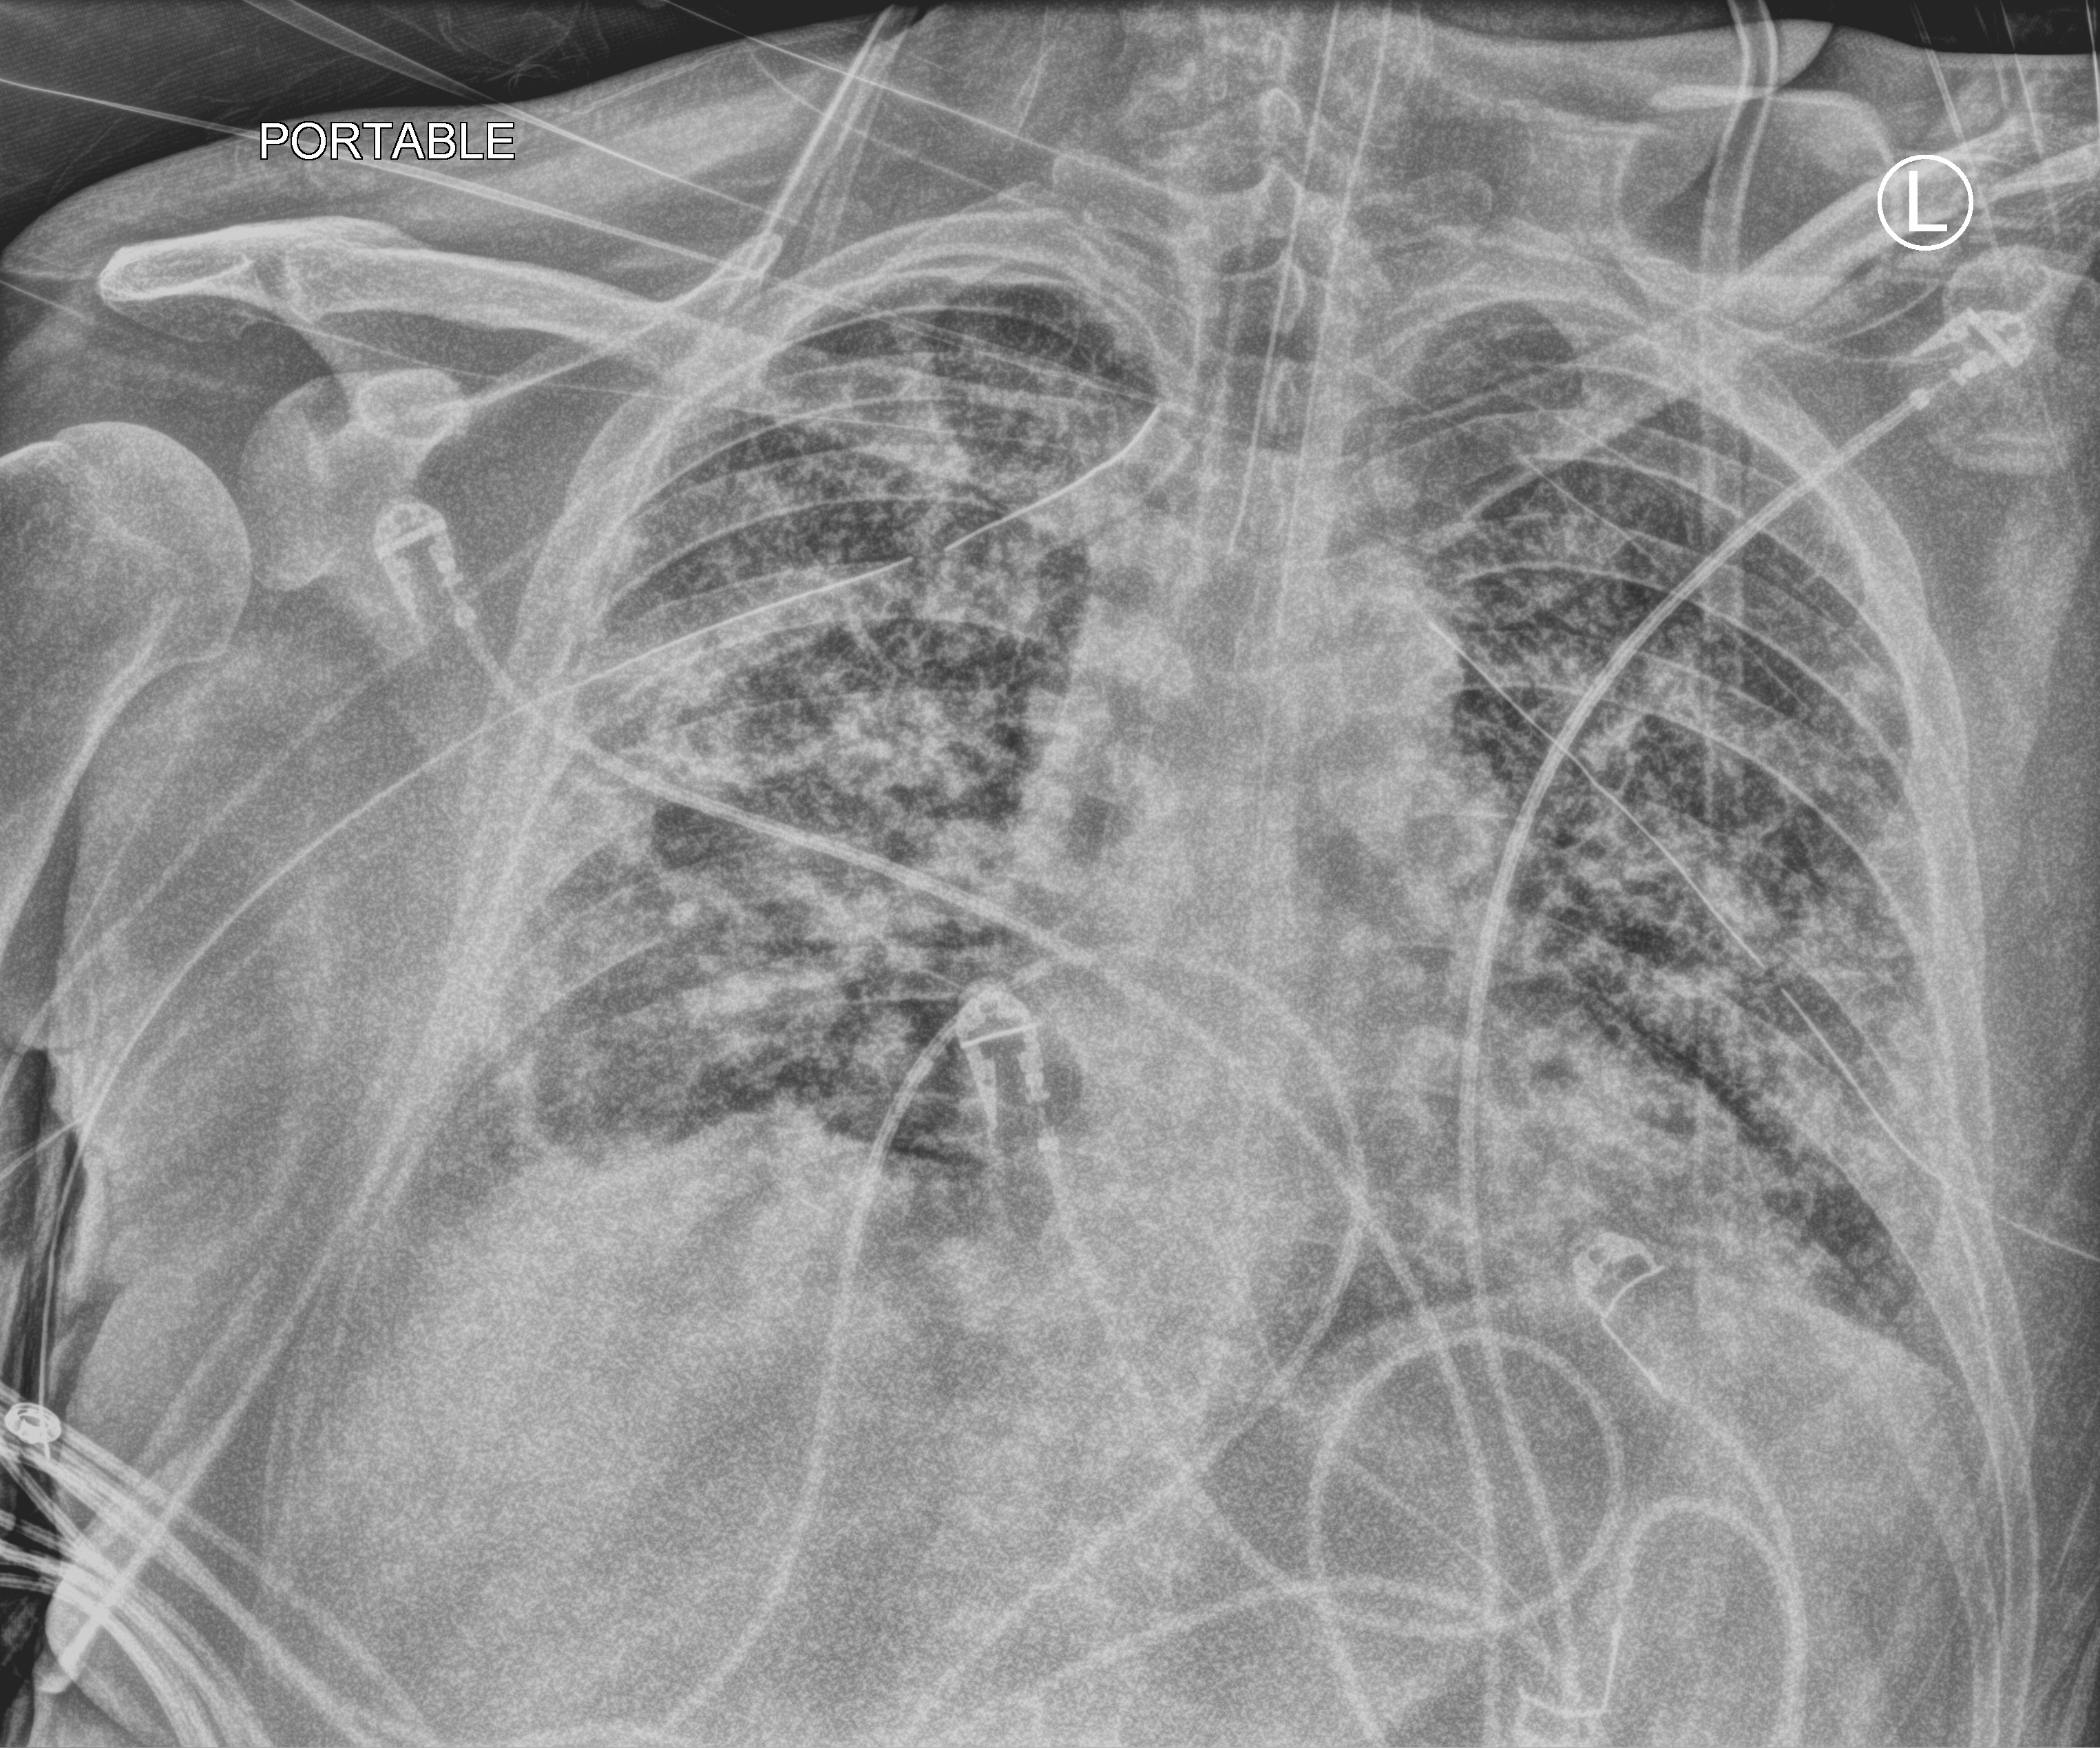
Portable chest radiograph; anteroposterior (AP) projection. Patient hospitalised with COVID-19; male, aged 18–59 years.
From the hospital-stay record, not from the radiograph (when in the stay this image was taken is not recorded): chronic kidney disease (admission record): no.